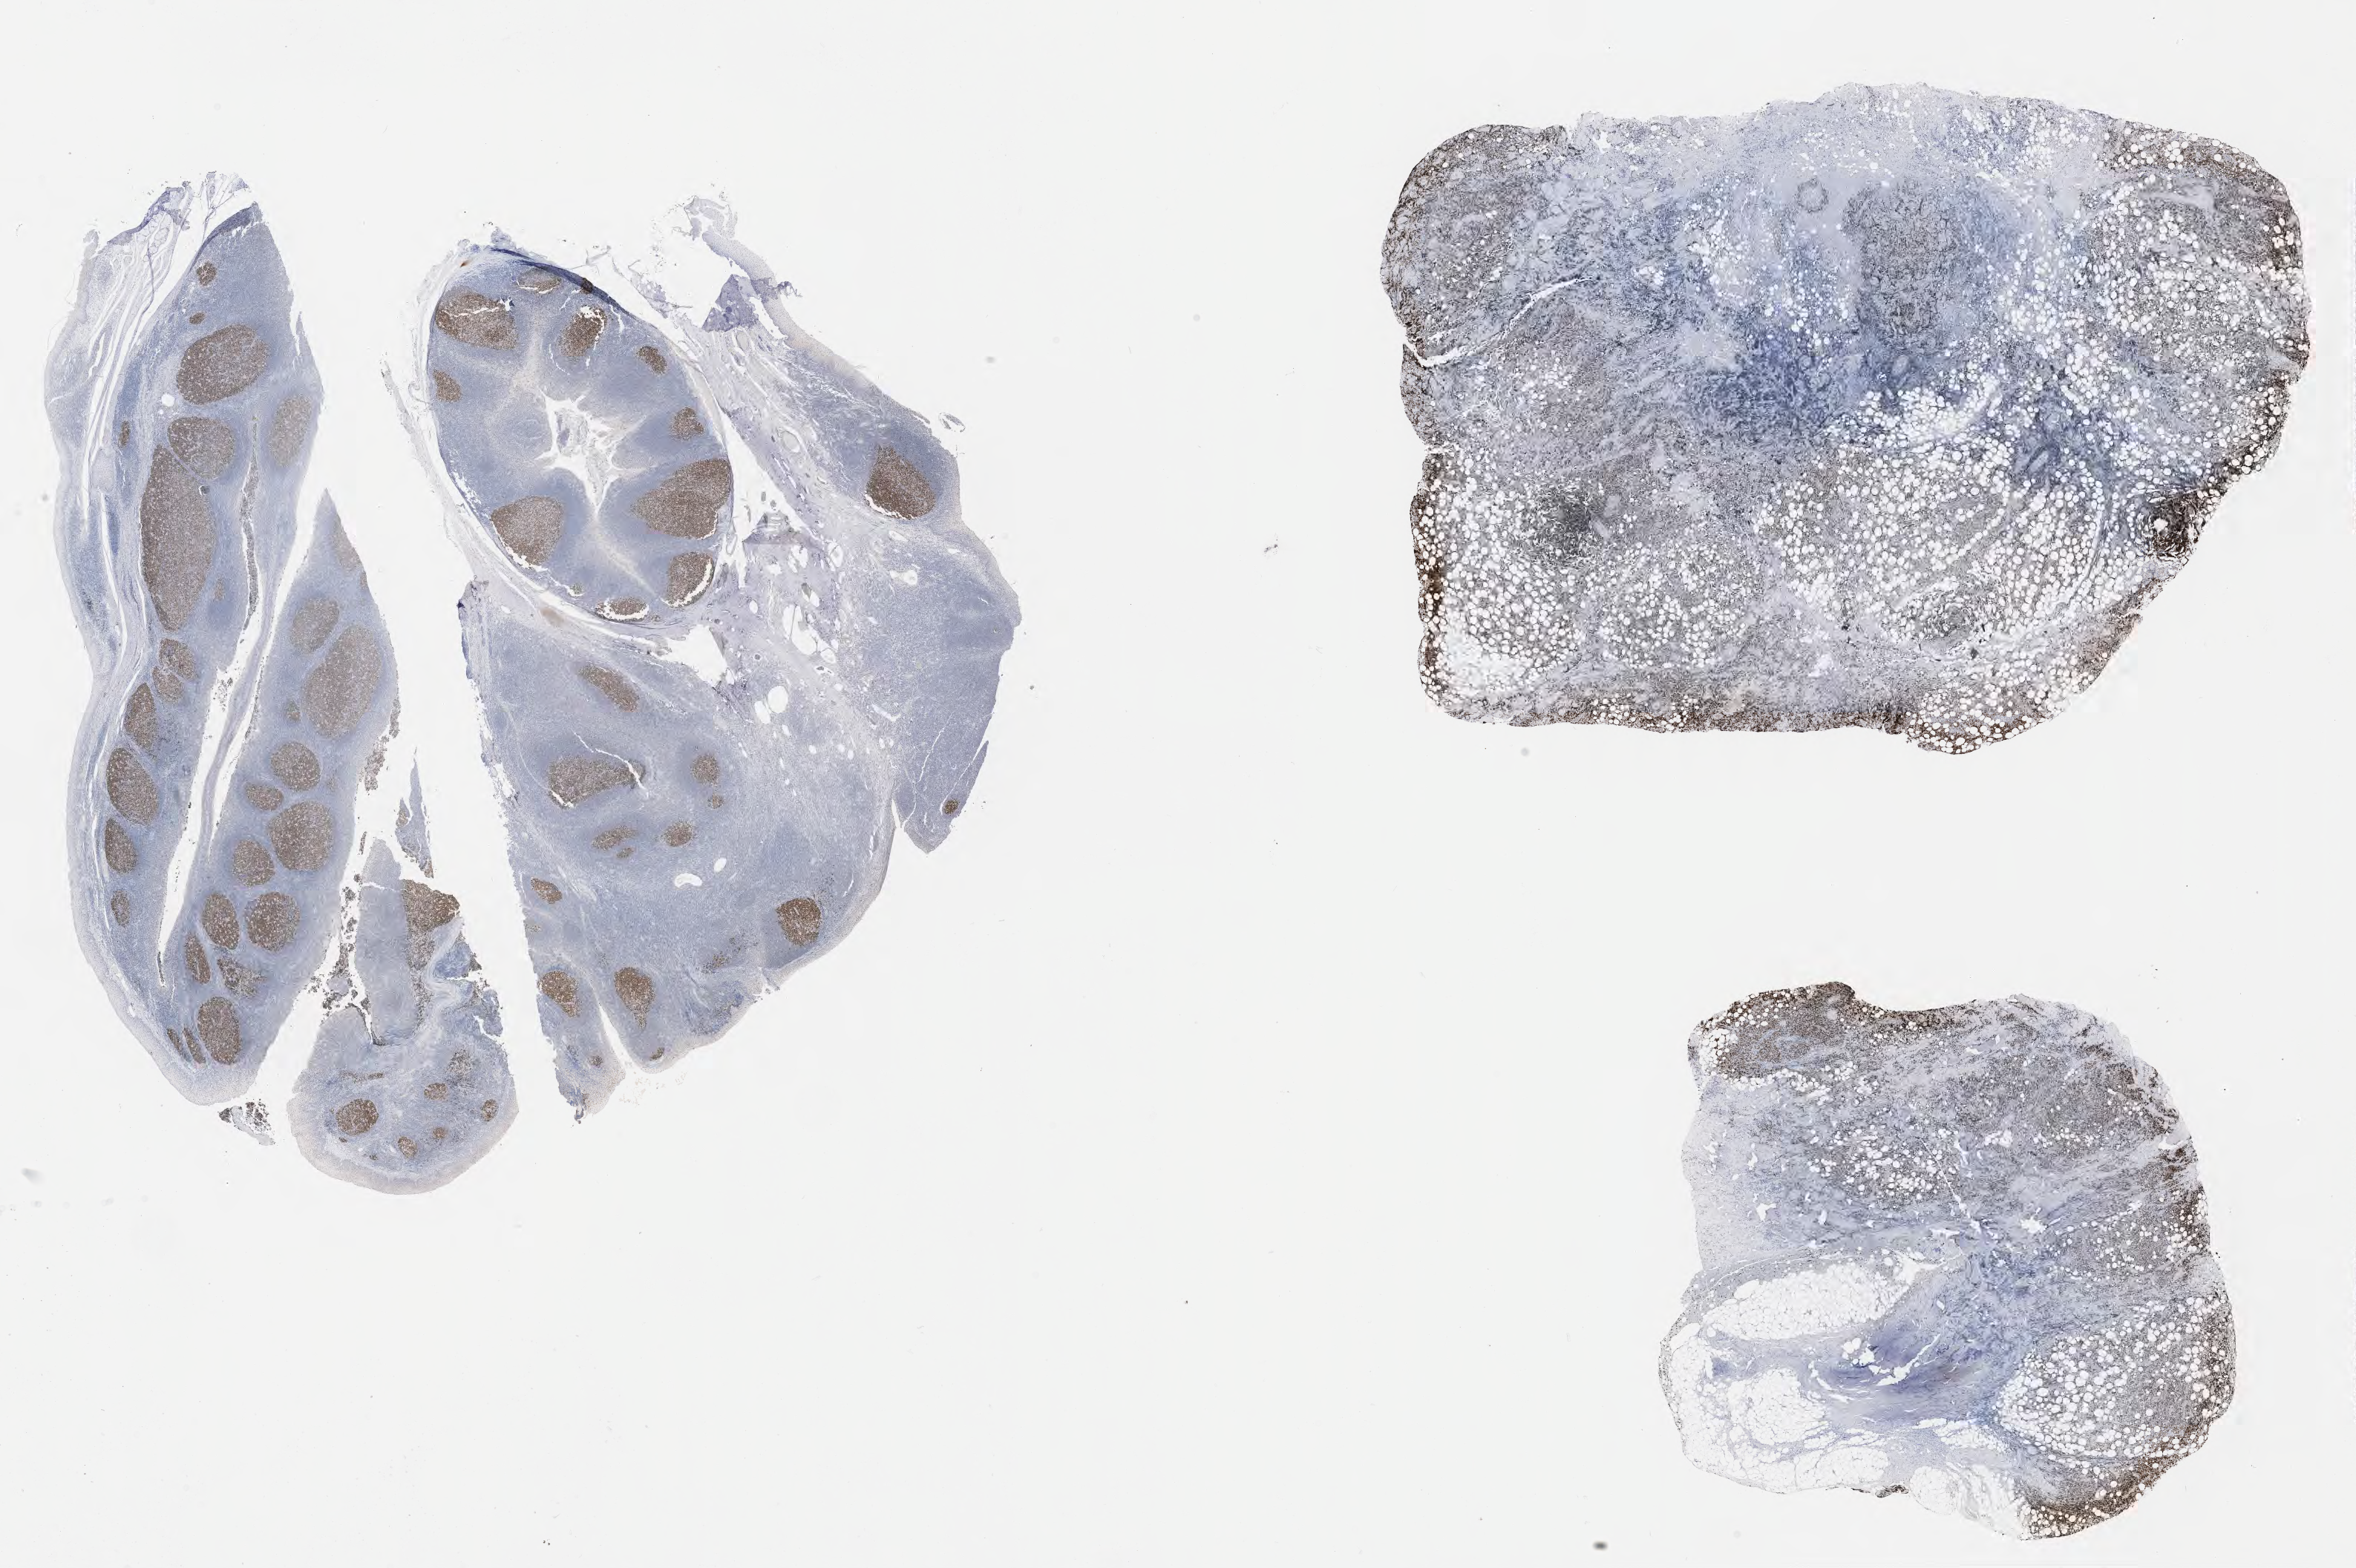
Immunohistochemistry (IHC) whole-slide image stained for BCL6 — shown as a low-resolution overview of the whole scanned area (about 25.7 x 17.1 mm), specimen: tumor tissue, anatomic site: kidney. Patient: male, aged 63.
Histologic diagnosis: Diffuse large B-cell lymphoma, NOS.